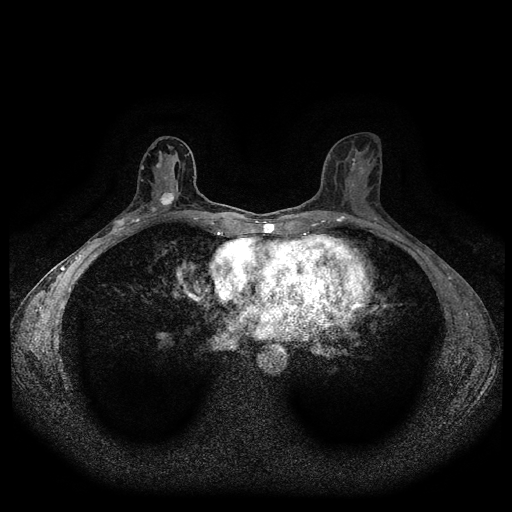
Breast MRI (dynamic contrast-enhanced, multi-phase), one axial slice. Position 53 of 116 along the scan axis. Dynamic contrast-enhanced series, time point 2 of 5 at this slice position (early post-contrast). 1.5 T. TE 2.6 ms, TR 5.3 ms. 2 mm slice thickness. 512 × 512 image matrix, field of view 350 × 350 mm. Female patient, age 50 years.
Structures marked on this image (semi-automatic segmentation, software-assisted and operator-edited):
- breast lesion (labelled 'tumour' in the annotation; benign lesions carry a separate 'benign' label): bounding box (x1, y1, x2, y2) in pixels: (149, 189, 177, 216)